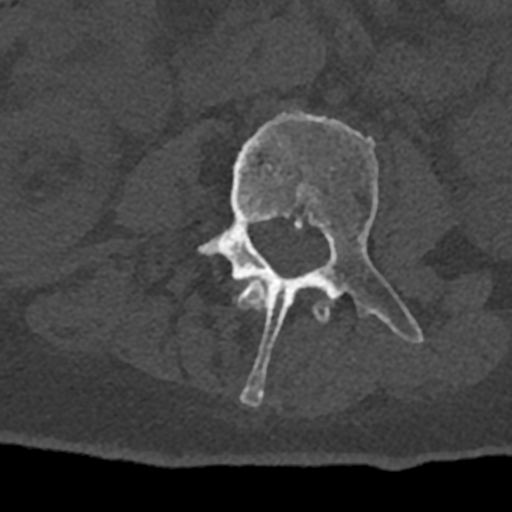
CT including the spine, one axial slice. Position 320 of 797 along the scan axis. Reconstruction kernel Br40s/3. 120 kVp. Bone window (W 1800 / L 400 HU). 0.5 mm slice thickness. 512 × 512 image matrix, field of view 160 × 160 mm. Patient: male, 74 years. Case-level facts recorded for this patient, not image findings: primary cancer: renal; vertebrae with lytic lesions (as recorded): T10, L1, L2, L3, L4, L5.
Annotated regions visible in this slice (semi-automatic segmentation, software-assisted and operator-edited):
- L2 vertebra: bounding box [x1, y1, x2, y2] px = [234, 280, 330, 323]
- L3 vertebra: [195, 109, 424, 406]